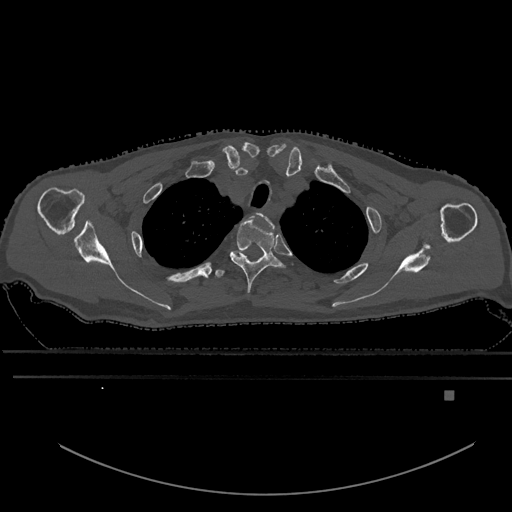
CT including the spine, one axial slice. Position 492 of 969 along the scan axis. Bone window (W 1800 / L 400 HU). 512 × 512 image matrix, field of view 456 × 456 mm. Male patient, age 82 years. From the clinical record (not read from this slice): primary cancer: prostate; vertebrae with lytic lesions (as recorded): T11, T9, T8, T2.
Annotated regions visible in this slice (semi-automatic segmentation, software-assisted and operator-edited):
- T1 vertebra: box from (x=256, y=213) to (x=274, y=227) px
- T2 vertebra: (x=230, y=218)–(x=287, y=295)
- T3 vertebra: (x=214, y=269)–(x=226, y=279)